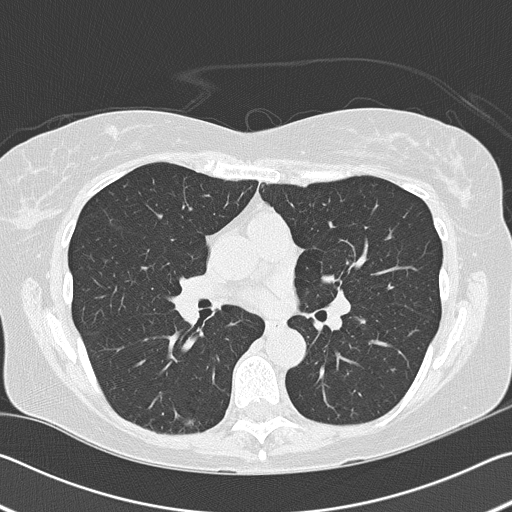
Low-dose screening chest CT, axial slice; baseline annual screen; lung window (W 1500 / L -600 HU); lung (sharp) reconstruction kernel (B50f); 120 kVp; slice 73 of 159 in the series. Female participant, aged 60 years at enrolment. Former smoker at enrolment.
- Expert reader's lesion annotation, bounding box (x1, y1, x2, y2) in pixels: (171, 408, 218, 446).
- The screening reader recorded 2 non-calcified nodules or masses ≥4 mm on this exam (right lower lobe, right middle lobe); which of them this box marks is not recorded.
- Official screen result: positive, change unspecified: nodule(s) >= 4 mm or enlarging nodule(s), mass(es), or other non-specific abnormalities suspicious for lung cancer.
- Participant outcome: lung cancer diagnosed 799 days after this screen — acinar cell carcinoma, right lower lobe, moderately differentiated (G2), stage IA (AJCC 6th edition), 10 mm at pathology.